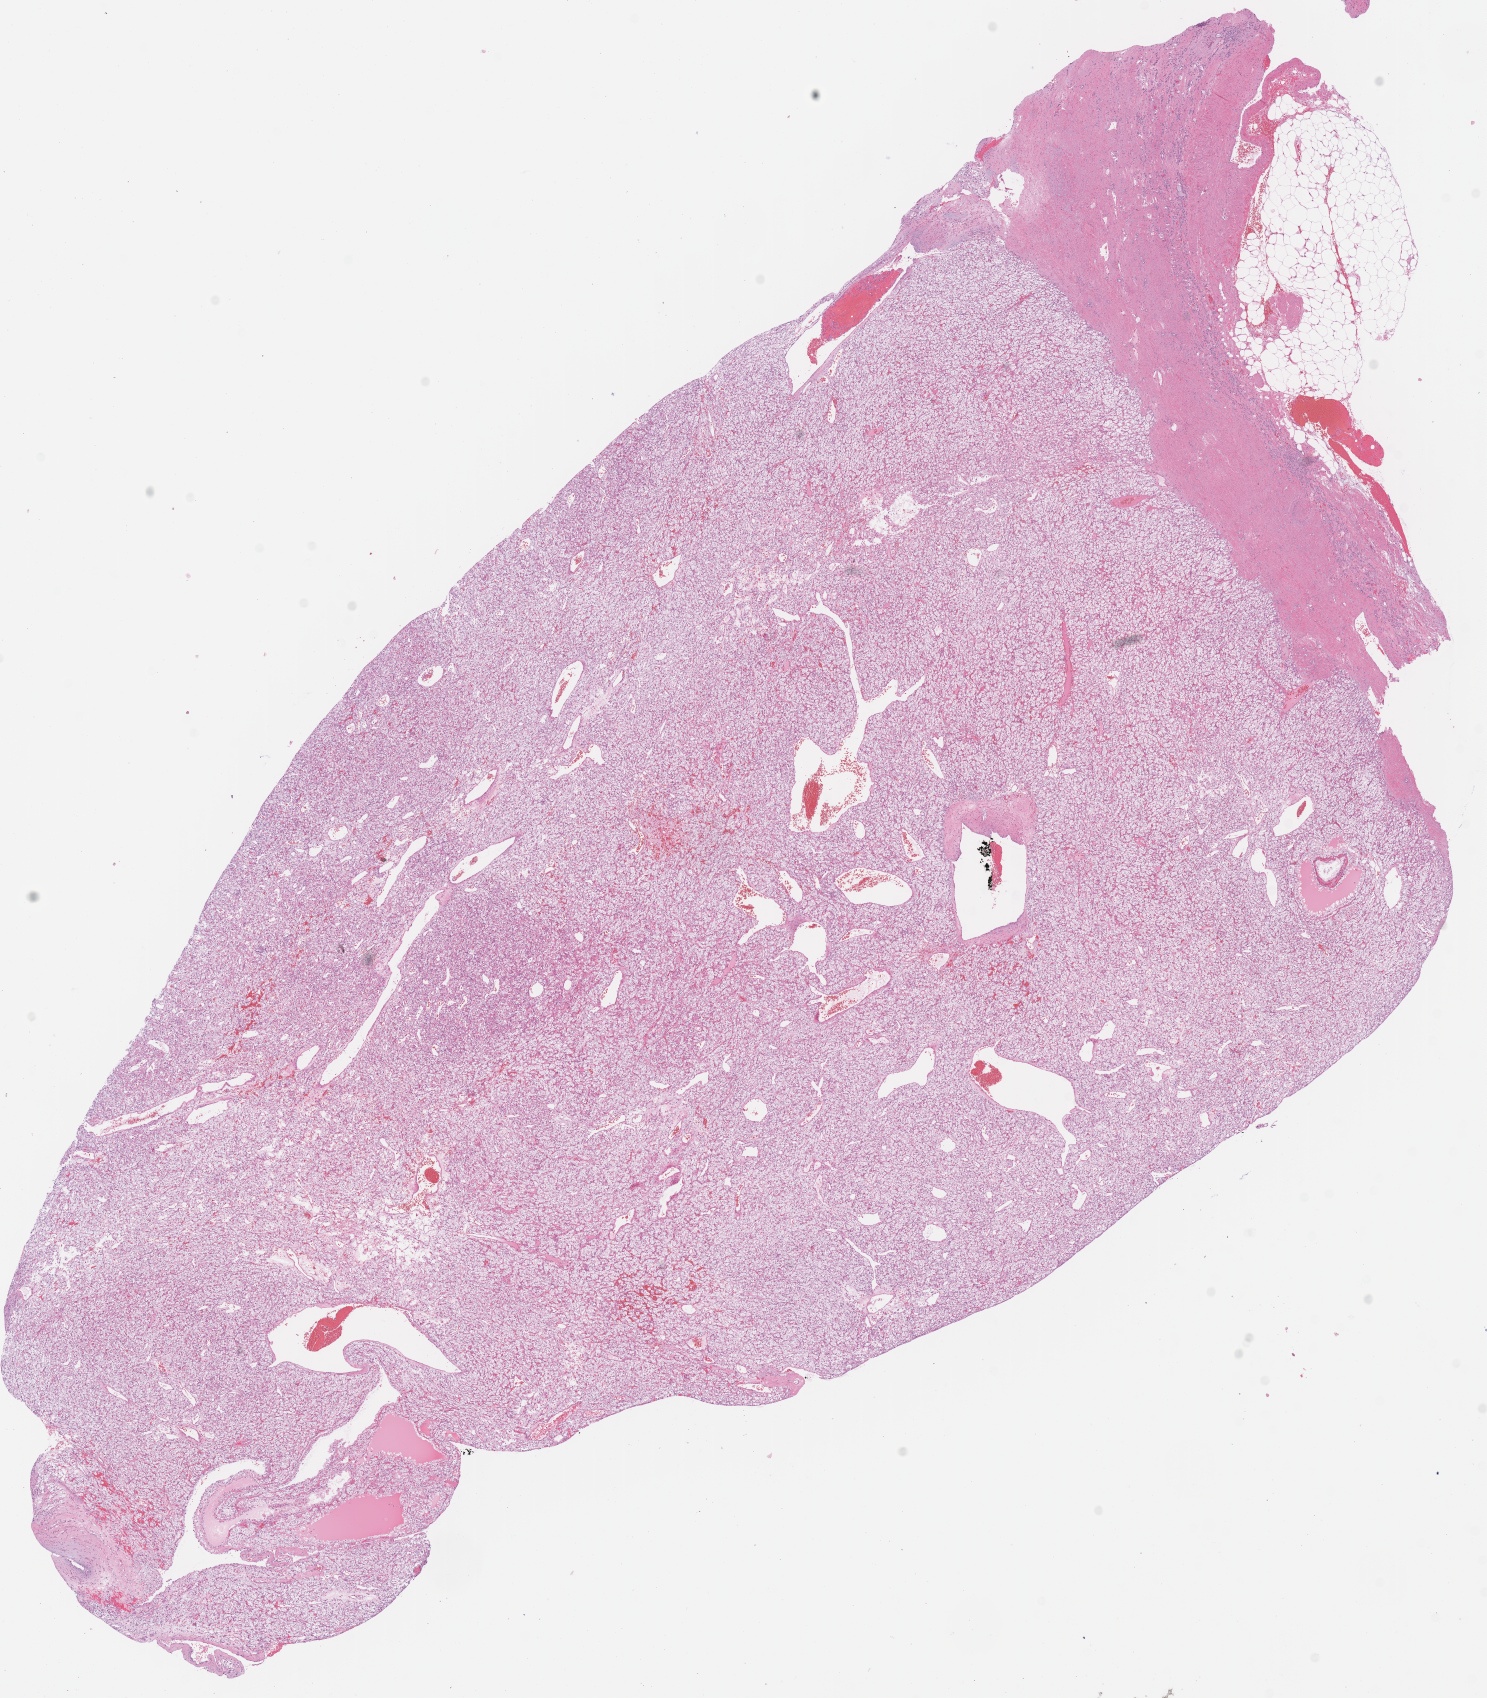
Digitized H&E-stained tissue section (whole slide) — a low-resolution overview of the entire scanned area, about 11.7 x 13.4 mm (slide scanned at 40x); formalin-fixed paraffin-embedded (FFPE) diagnostic section; kidney, primary tumour sample. Male patient; age at initial diagnosis 66 years. Histologic grade: G3 (poorly differentiated).
AJCC pathologic stage: III. Diagnosis: Clear cell adenocarcinoma, NOS.